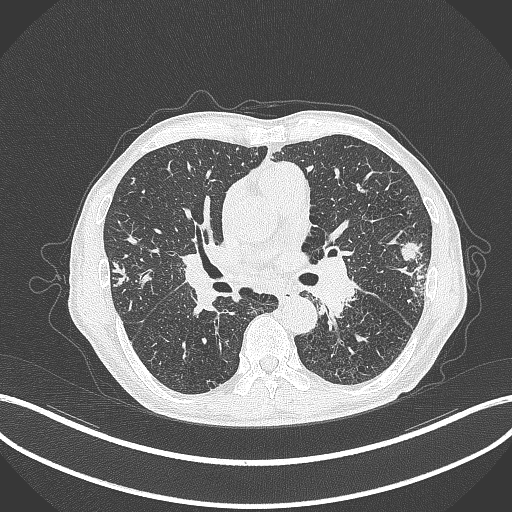
Chest CT, one axial slice. Slice 219 of 463 in the series (ordered by position). Reconstruction kernel B70f. 120 kVp. Lung window (W 1500 / L -600 HU). 1 mm slice thickness. 512 × 512 image matrix, field of view 400 × 400 mm. Male patient, age 74 years. From the clinical record (not read from this slice): clinical TNM (as recorded): T2a N1 M0.
Structures marked on this image (bounding box drawn by a radiologist):
- lung tumour (recorded histology: adenocarcinoma): box from (x=399, y=239) to (x=427, y=268) px